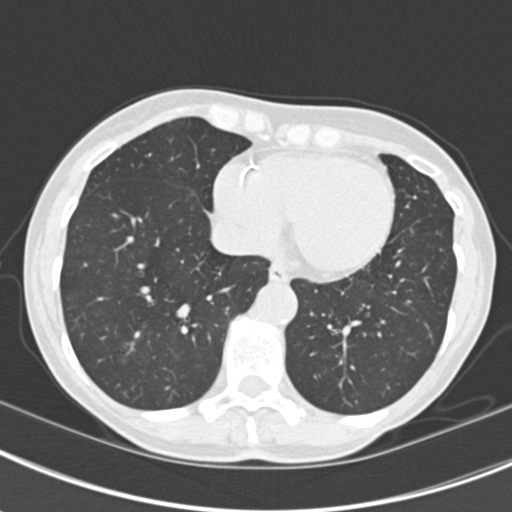
Axial slice from a low-dose chest CT screening exam, second screening round (one year after baseline), lung window (W 1500 / L -600 HU), standard (soft-tissue) reconstruction kernel (B30f), slice 138 of 219 in the series. Female, age 63 years at enrolment.
Expert reader's lesion annotation, bounding box (x1, y1, x2, y2) in pixels: (107, 327, 151, 369). The screening reader recorded 9 non-calcified nodules or masses ≥4 mm on this exam (left upper lobe, right upper lobe, left upper lobe, left lower lobe, right middle lobe, left lower lobe, left lower lobe, right lower lobe, right lower lobe); which of them this box marks is not recorded. Official screen result: positive, other. Later outcome: lung cancer diagnosed 408 days after this screen — bronchiolo-alveolar adenocarcinoma, NOS, right upper lobe, right middle lobe, right lower lobe, left upper lobe, left lower lobe, moderately differentiated (G2), stage IV (AJCC 6th edition).